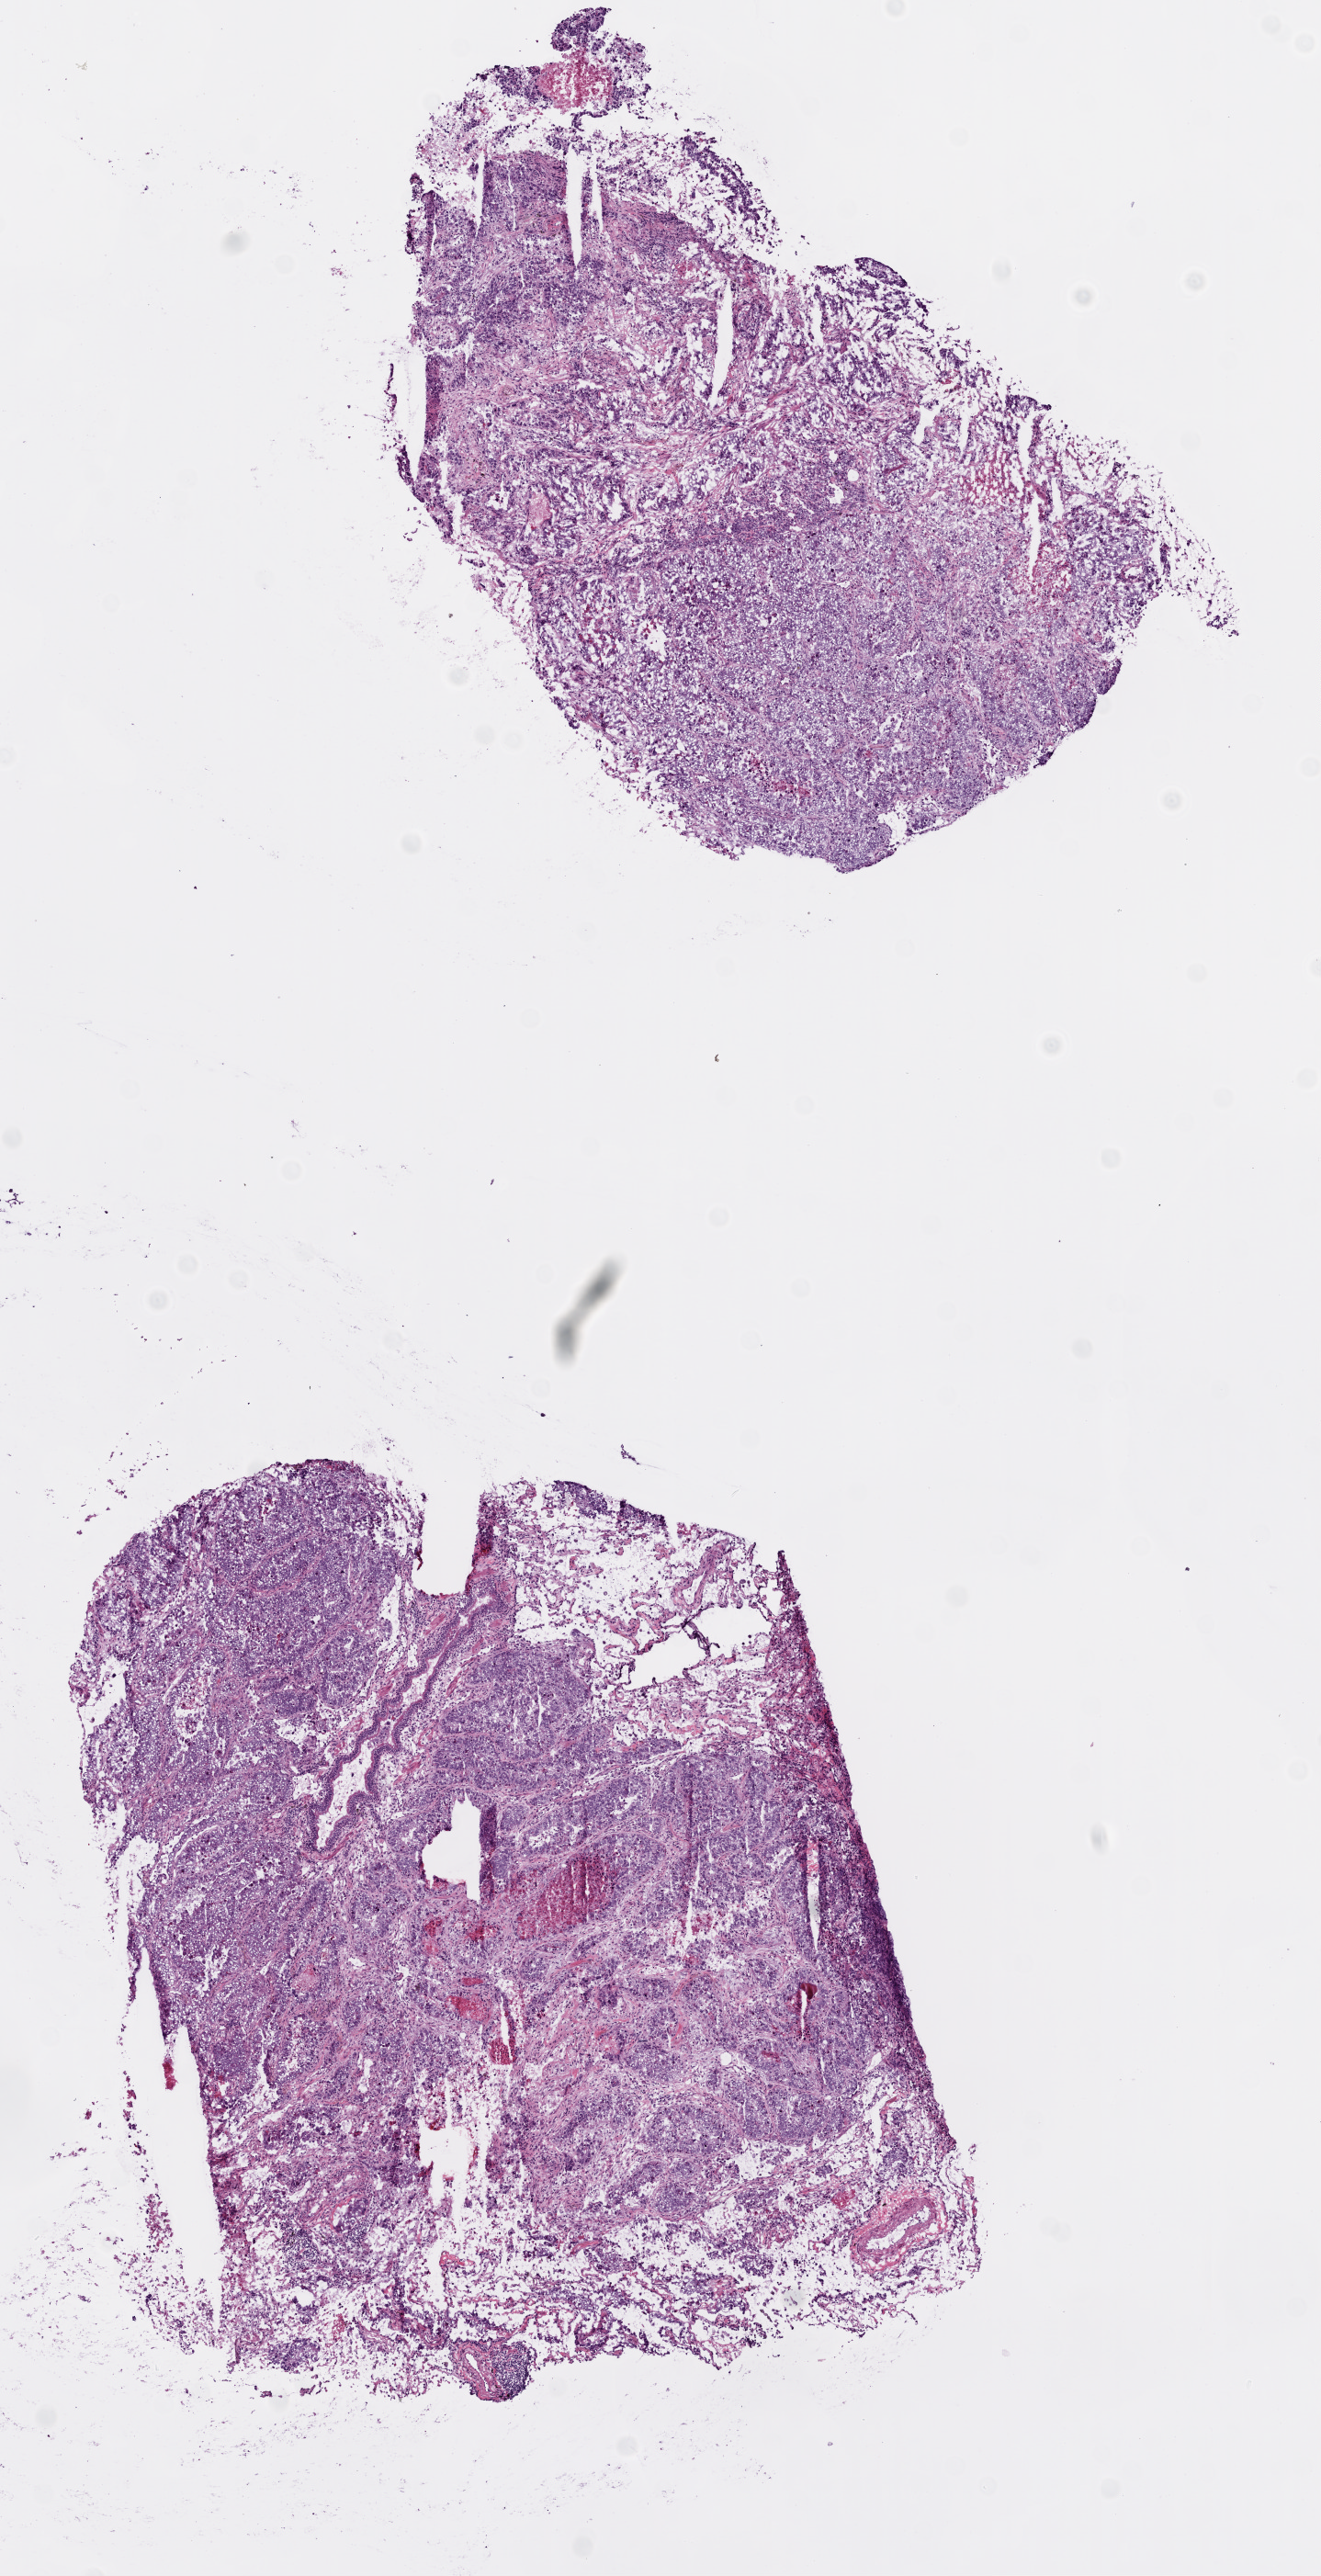
Whole-slide histology image, H&E — whole scanned area (about 5.8 x 11.3 mm, slide scanned at 20x) shown as a low-resolution overview; frozen section; sample: primary tumour, lung. Female, age 47 years at initial diagnosis.
AJCC pathologic stage: IIA (7th edition). Pathologic diagnosis: Adenocarcinoma, NOS.